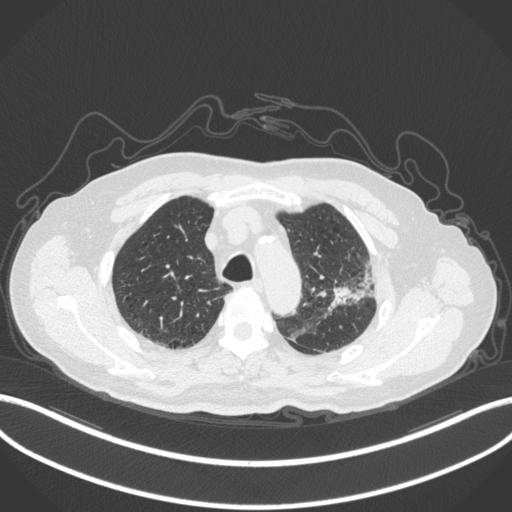
Chest CT, one axial slice. Position 235 of 331 along the scan axis. Lung window (W 1500 / L -600 HU). 1 mm slice thickness. 512 × 512 image matrix, field of view 400 × 400 mm. Male patient, age 79 years. From the clinical record (not read from this slice): clinical TNM (as recorded): T2a N1 M1; histopathological grade: G3.
Structures marked on this image (rectangle marked by the reading radiologist):
- lung tumour (recorded histology: adenocarcinoma): bounding box (x1, y1, x2, y2) in pixels: (328, 259, 372, 318)